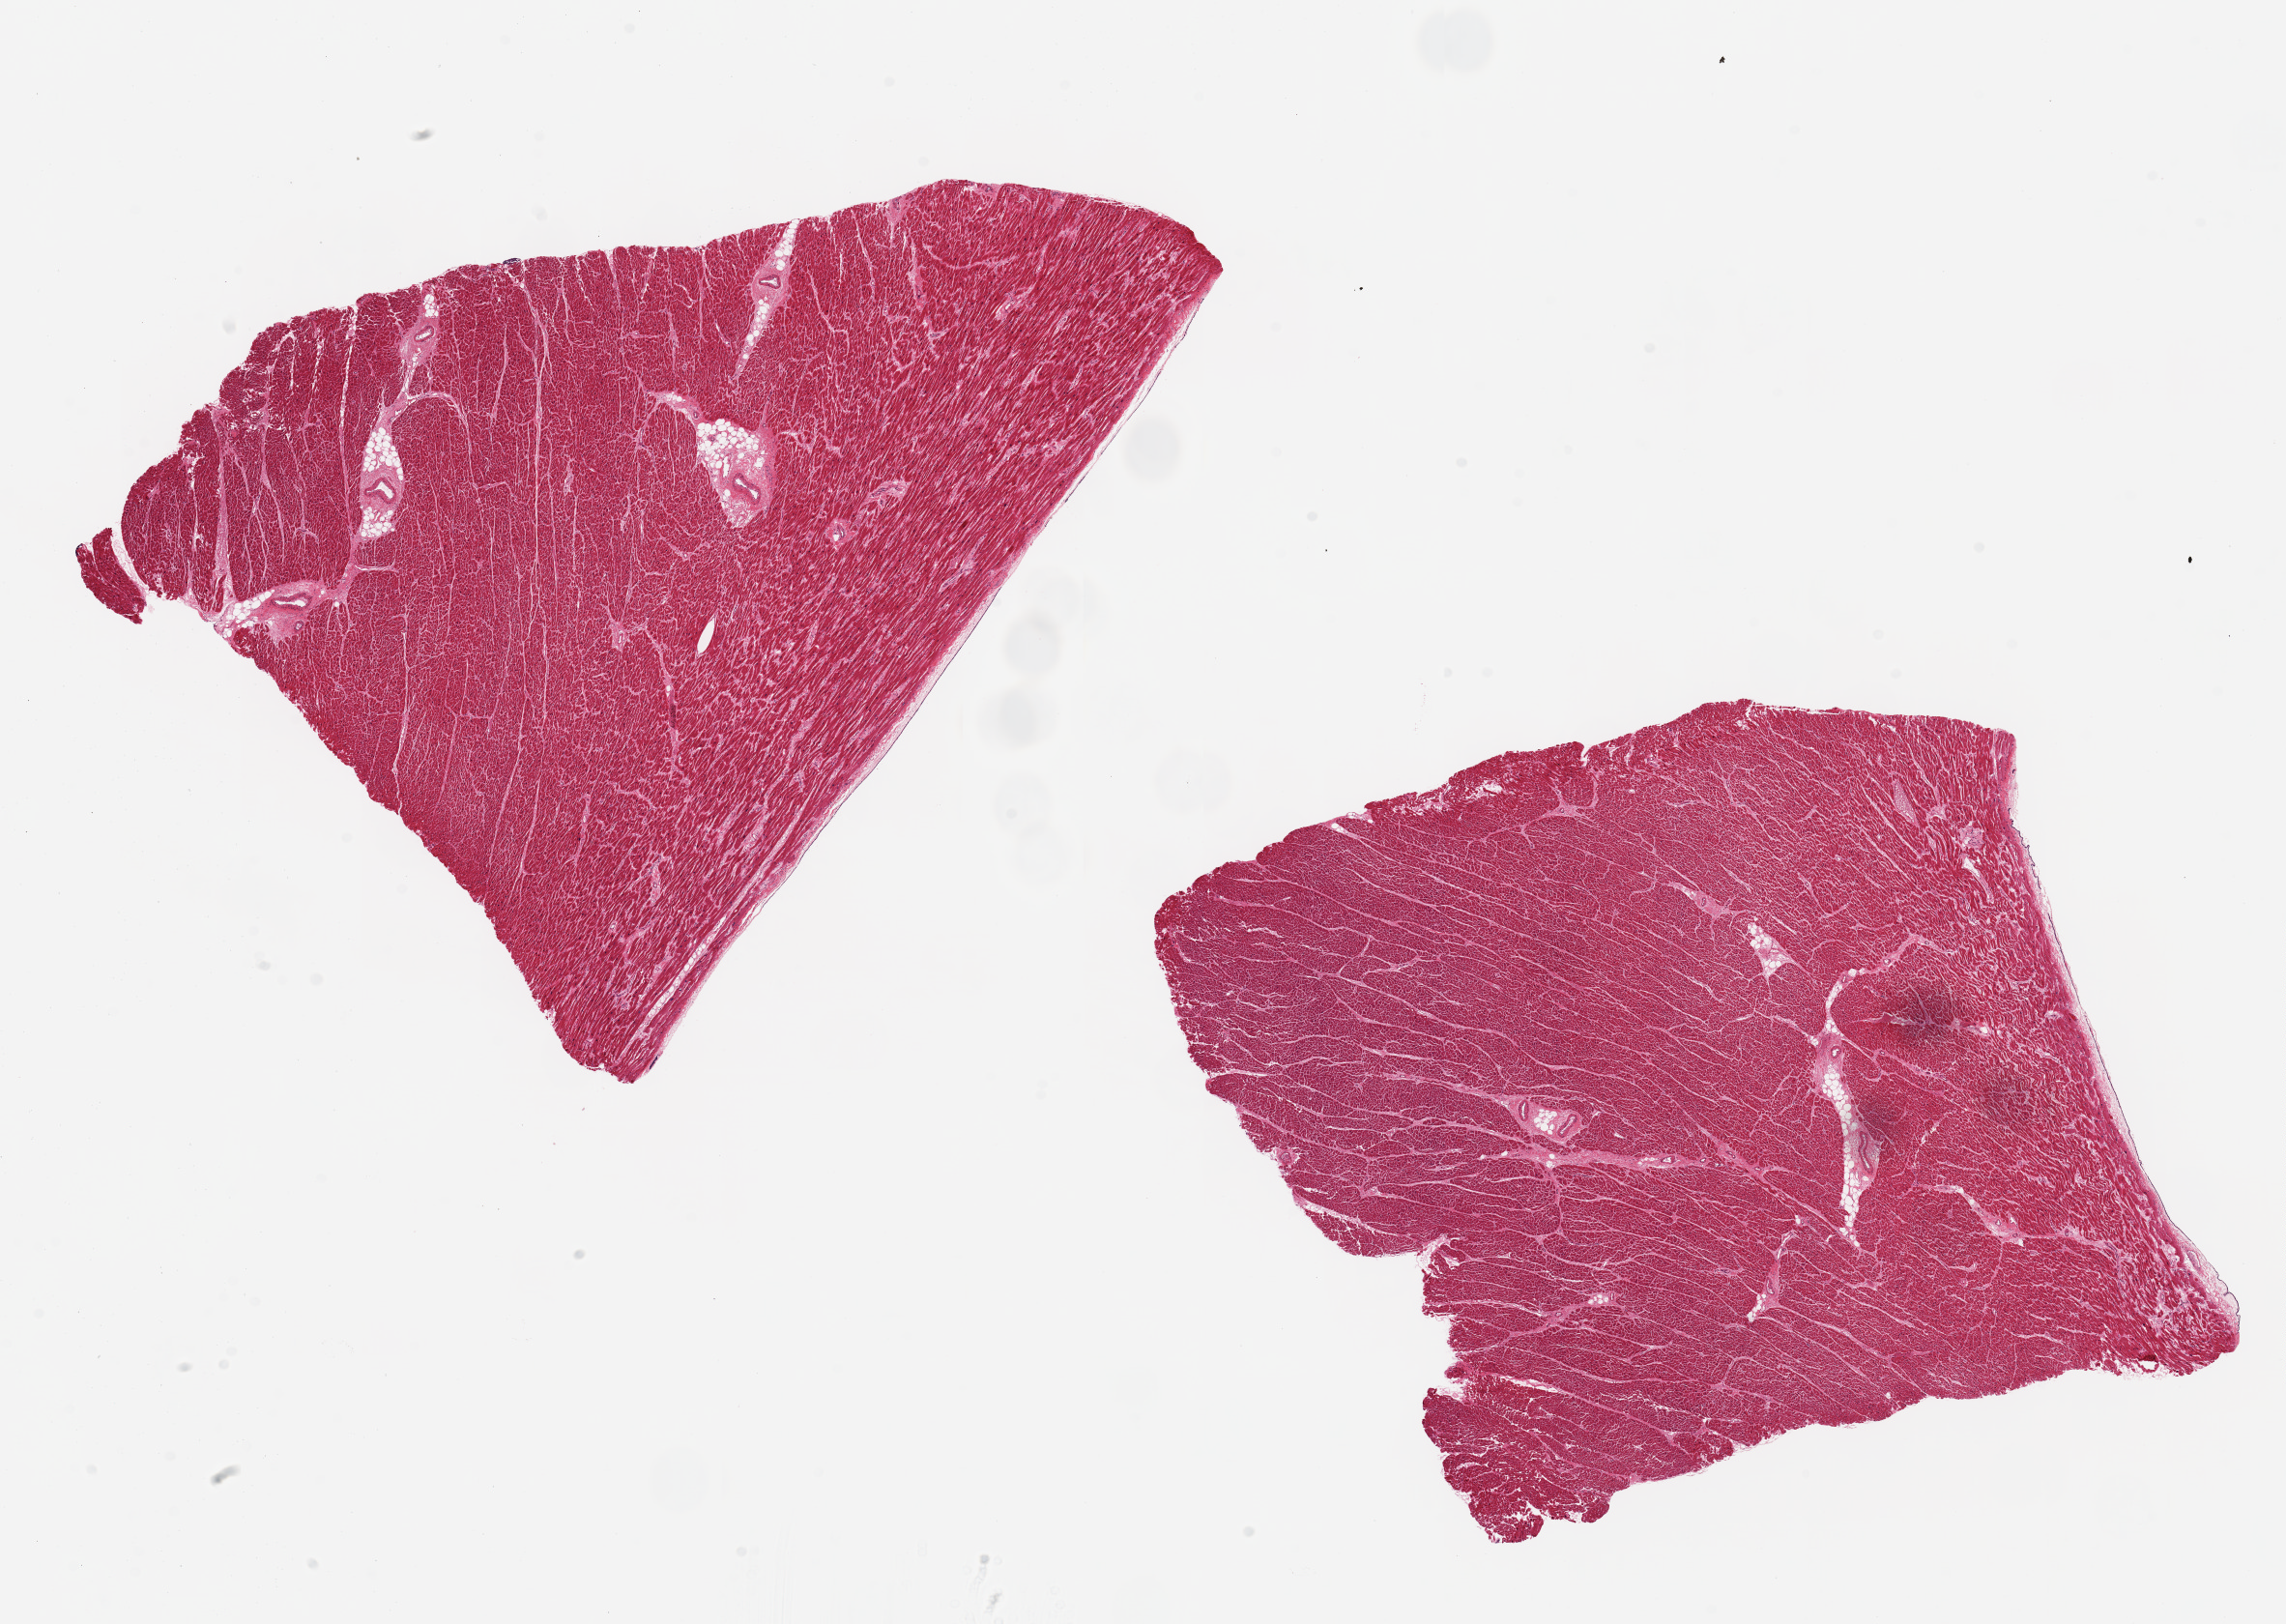
Whole-slide image, H&E stain — a low-resolution overview of the entire scanned area, about 18.7 x 13.3 mm (from a 20x scan), PAXgene-fixed paraffin-embedded (PFPE) section, section of heart (target tissue), donor tissue sample. Donor sex: male.
Pathologist's review note for this sample: 2 ~7.5x5.5mm aliquots, early ischemic changes (contraction bands).